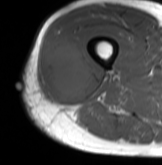
MRI of an extremity soft-tissue mass, one axial slice; position 31 of 61 along the scan axis; MR volume resampled by the dataset authors to the PET/CT grid (not the native acquisition matrix); 3.27 mm slice thickness; 162 × 165 image matrix, field of view 158 × 161 mm. Male patient. Case-level facts recorded for this patient, not image findings: histological type: poorly differentiated synovial sarcoma; grade: high; site of the primary tumour: right buttock.
Annotated regions visible in this slice (expert contour drawn on MRI and transferred to this co-registered scan by the dataset authors):
- gross tumour volume including surrounding oedema: bounding box [x1, y1, x2, y2] px = [41, 31, 95, 101]
- gross tumour volume (mass): [45, 40, 95, 101]